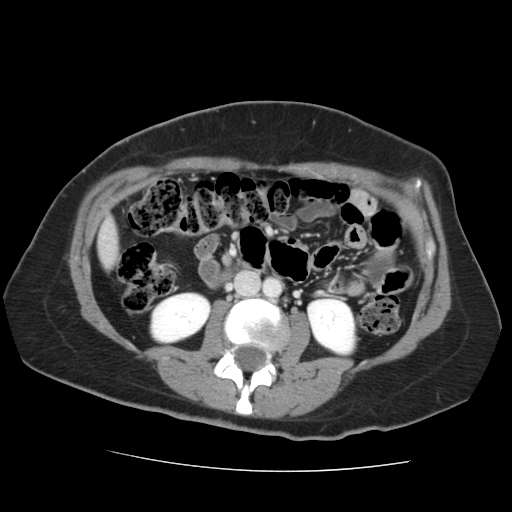
Contrast-enhanced abdominal CT, one axial slice. Slice 41 of 144 in the series (ordered by position). Soft-tissue window (W 400 / L 40 HU). 512 × 512 image matrix, field of view 333 × 333 mm. Female patient, age 46 years. Case-level facts recorded for this patient, not image findings: diagnosis: colorectal cancer liver metastases, imaged before liver resection; multiple liver metastases: no; largest metastasis: 2.8 cm.
Outlined on this slice (manually delineated by an expert):
- liver: bounding box (x1, y1, x2, y2) in pixels: (99, 223, 118, 266)
- planned liver remnant (the part of the liver to remain after resection): (99, 245, 110, 266)